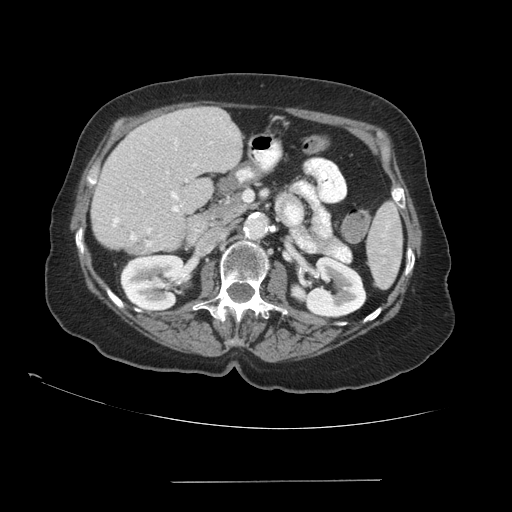
Contrast-enhanced abdominal CT (liver protocol), one axial slice; position 42 of 89 along the scan axis; reconstruction kernel STANDARD; soft-tissue window (W 400 / L 40 HU); 512 × 512 image matrix, field of view 400 × 400 mm. Case-level facts recorded for this patient, not image findings: diagnosis: hepatocellular carcinoma (patient treated with transarterial chemoembolisation; whether this scan precedes or follows treatment is not stated here); TNM stage (as recorded): Stage-IVA; Child-Pugh class: A.
Annotated regions visible in this slice (semi-automatic segmentation, software-assisted and operator-edited):
- liver parenchyma outside the tumour (the mass and vessels are separate outlines, so this box may not span the whole liver): bounding box (x1, y1, x2, y2) in pixels: (90, 106, 242, 248)
- liver vessels: (113, 141, 196, 240)